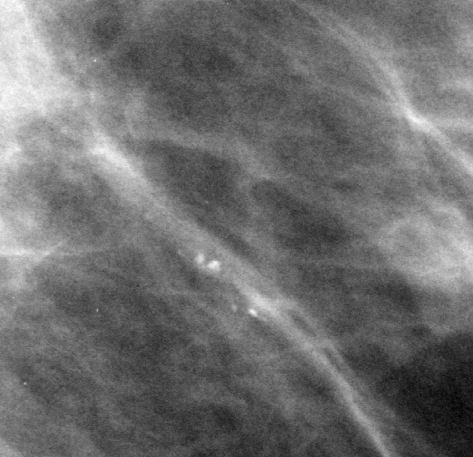
Cropped region of a digitized screen-film mammogram centred on a radiologist-marked abnormality, left breast, MLO view, BI-RADS breast density category 2 (scale 1–4).
Marked abnormality: calcifications, morphology punctate, distribution clustered; BI-RADS assessment category 4; subtlety rating 4 on a 1 (subtle) to 5 (obvious) scale; pathology result (as recorded, not read from the image): benign.